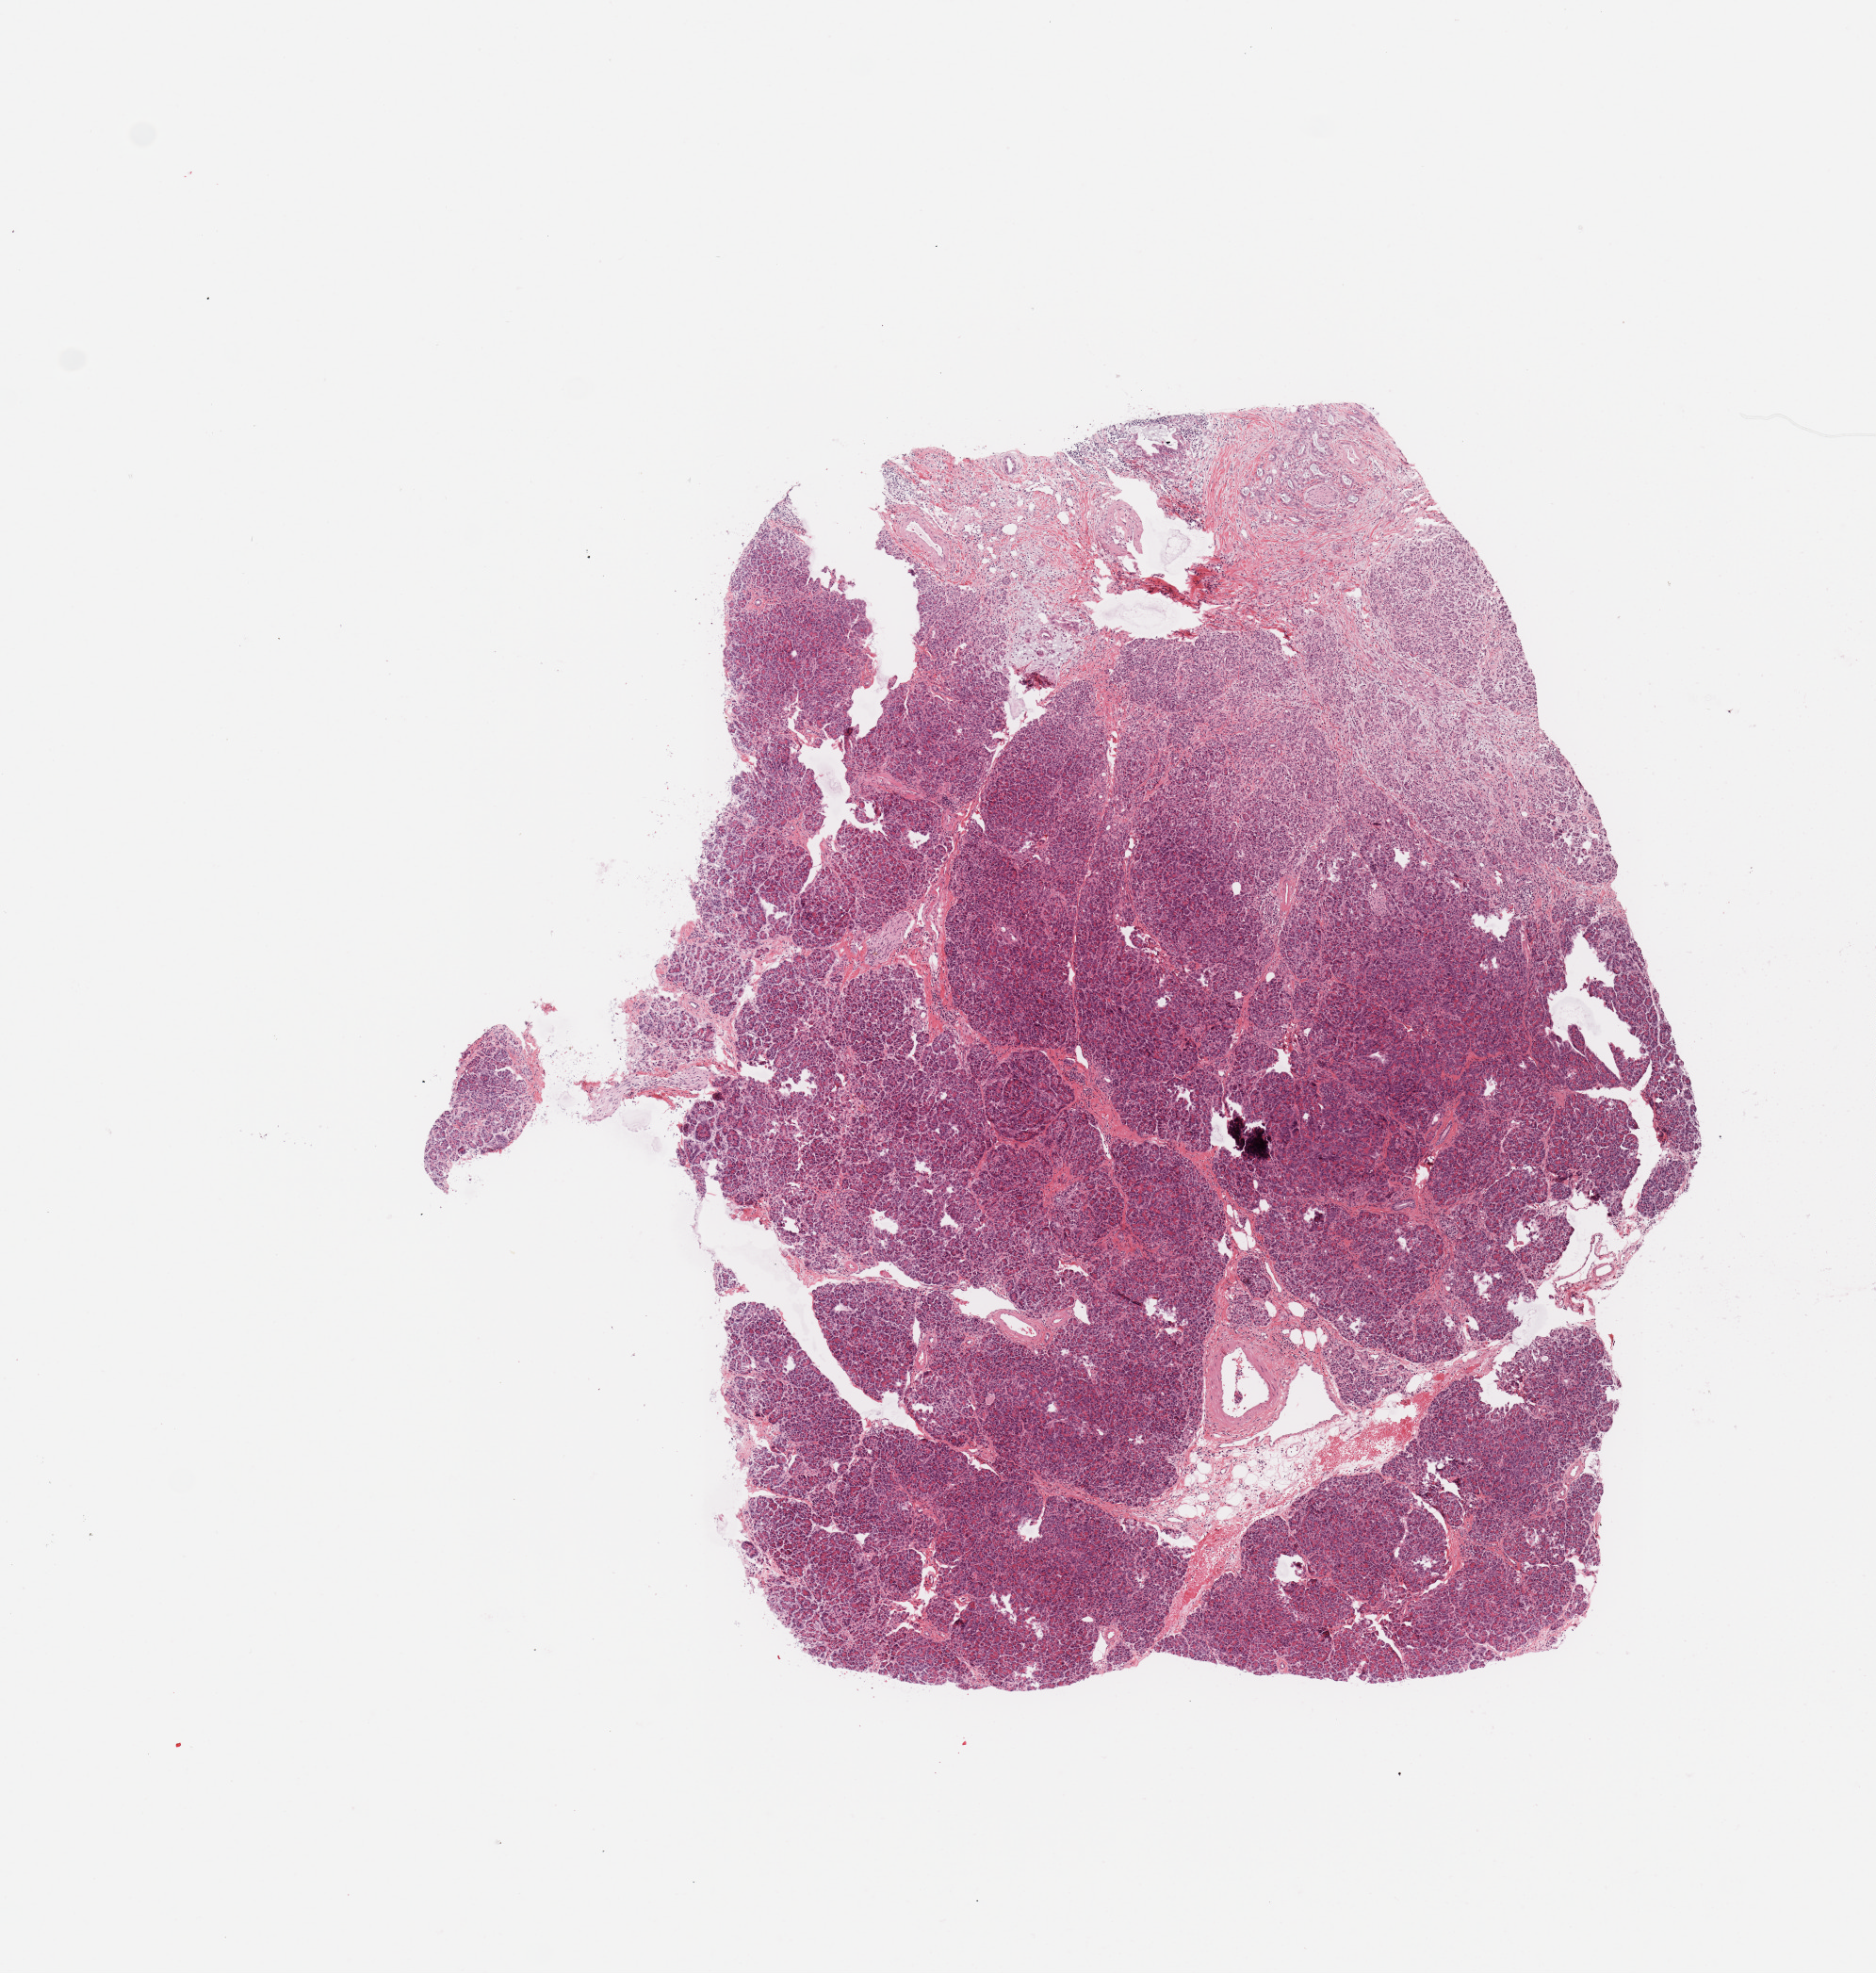
Whole-slide histology image, H&E, shown as a low-resolution overview of the whole scanned area (about 7.9 x 8.3 mm). Pancreas, normal (non-tumour) tissue. Patient: male, age 42 years.
This section: normal (non-tumour) tissue from the same patient. Patient diagnosis: Infiltrating duct carcinoma, NOS.